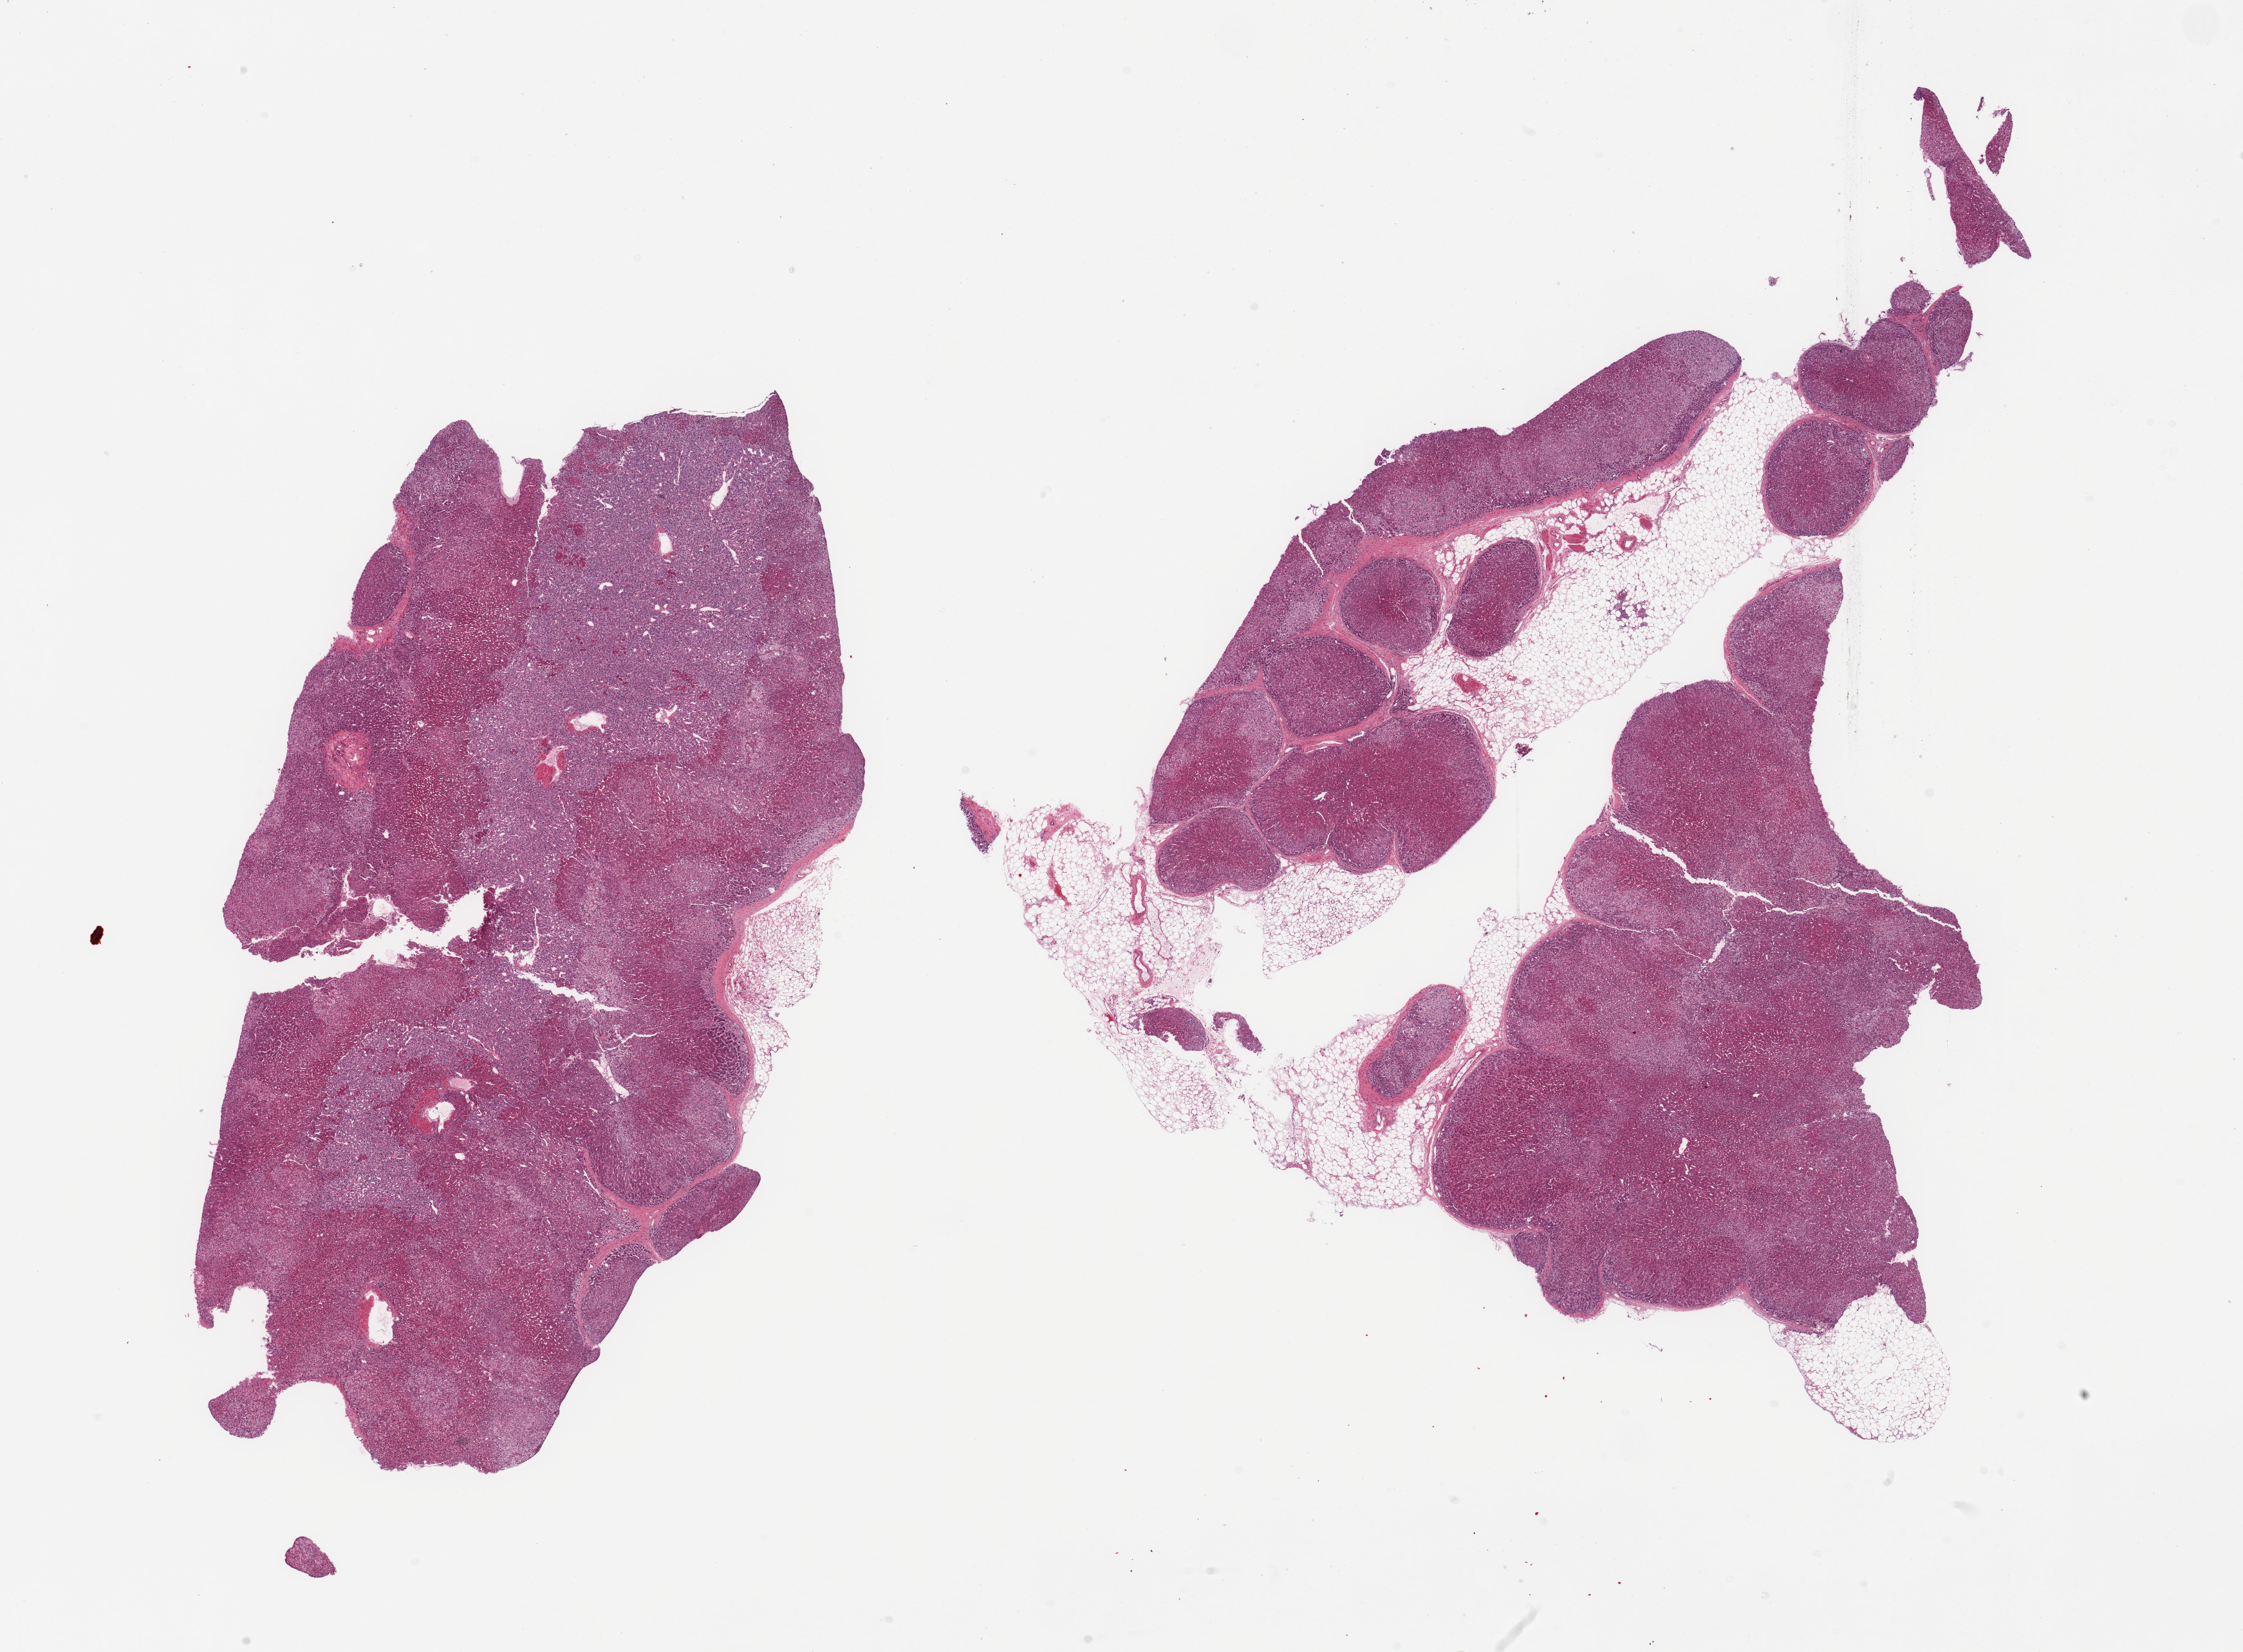
Digitized haematoxylin and eosin-stained section, shown as a low-resolution overview of the whole scanned area (about 27.6 x 20.3 mm, from a 20x scan); PAXgene-fixed, paraffin-embedded tissue; target tissue: adrenal gland; tissue donor sample. Female donor.
Reviewer comment on this tissue sample: 2 pieces; 1 with 30% external fat, other with 5% fat.